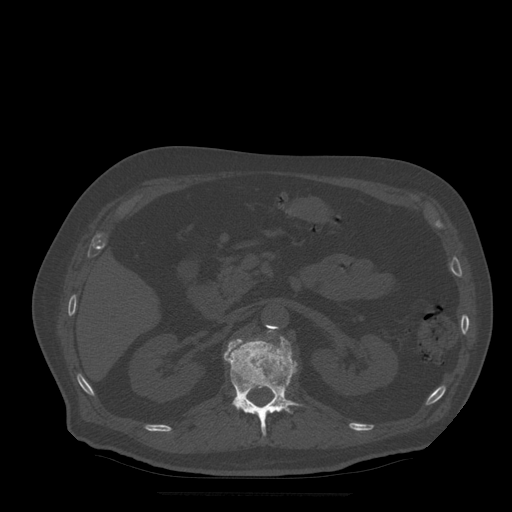
CT including the spine, one axial slice. Slice 194 of 522 in the series (ordered by position). Bone window (W 1800 / L 400 HU). 512 × 512 image matrix, field of view 420 × 420 mm. Patient age 72 years. From the clinical record (not read from this slice): primary cancer: prostate.
Structures marked on this image (semi-automatically segmented with operator editing):
- L1 vertebra: bounding box [x1, y1, x2, y2] px = [224, 336, 302, 436]
- L2 vertebra: [268, 330, 274, 333]